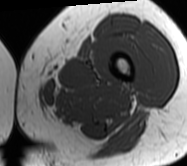
MRI of an extremity soft-tissue mass, one axial slice; MR volume resampled by the dataset authors to the PET/CT grid (not the native acquisition matrix); 3.27 mm slice thickness; 187 × 166 image matrix, field of view 183 × 162 mm. Female patient. Case-level facts recorded for this patient, not image findings: histological type: leiomyosarcoma; grade: high; site of the primary tumour: groin.
Outlined on this slice (expert contour drawn on MRI and transferred to this co-registered scan by the dataset authors):
- gross tumour volume including surrounding oedema: bounding box (x1, y1, x2, y2) in pixels: (18, 108, 21, 111)